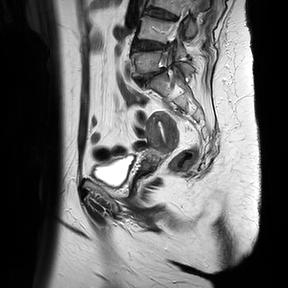
Pelvic MRI for cervical cancer, one sagittal slice. Position 23 of 37 along the scan axis. T2-weighted. 1.5 T. TE 100 ms, TR 4174.1 ms. 4 mm slice thickness. 288 × 288 image matrix. Female patient, age 65 years.
Annotated regions visible in this slice (manually delineated by an expert):
- uterus and cervix: bounding box (x1, y1, x2, y2) in pixels: (141, 111, 180, 171)